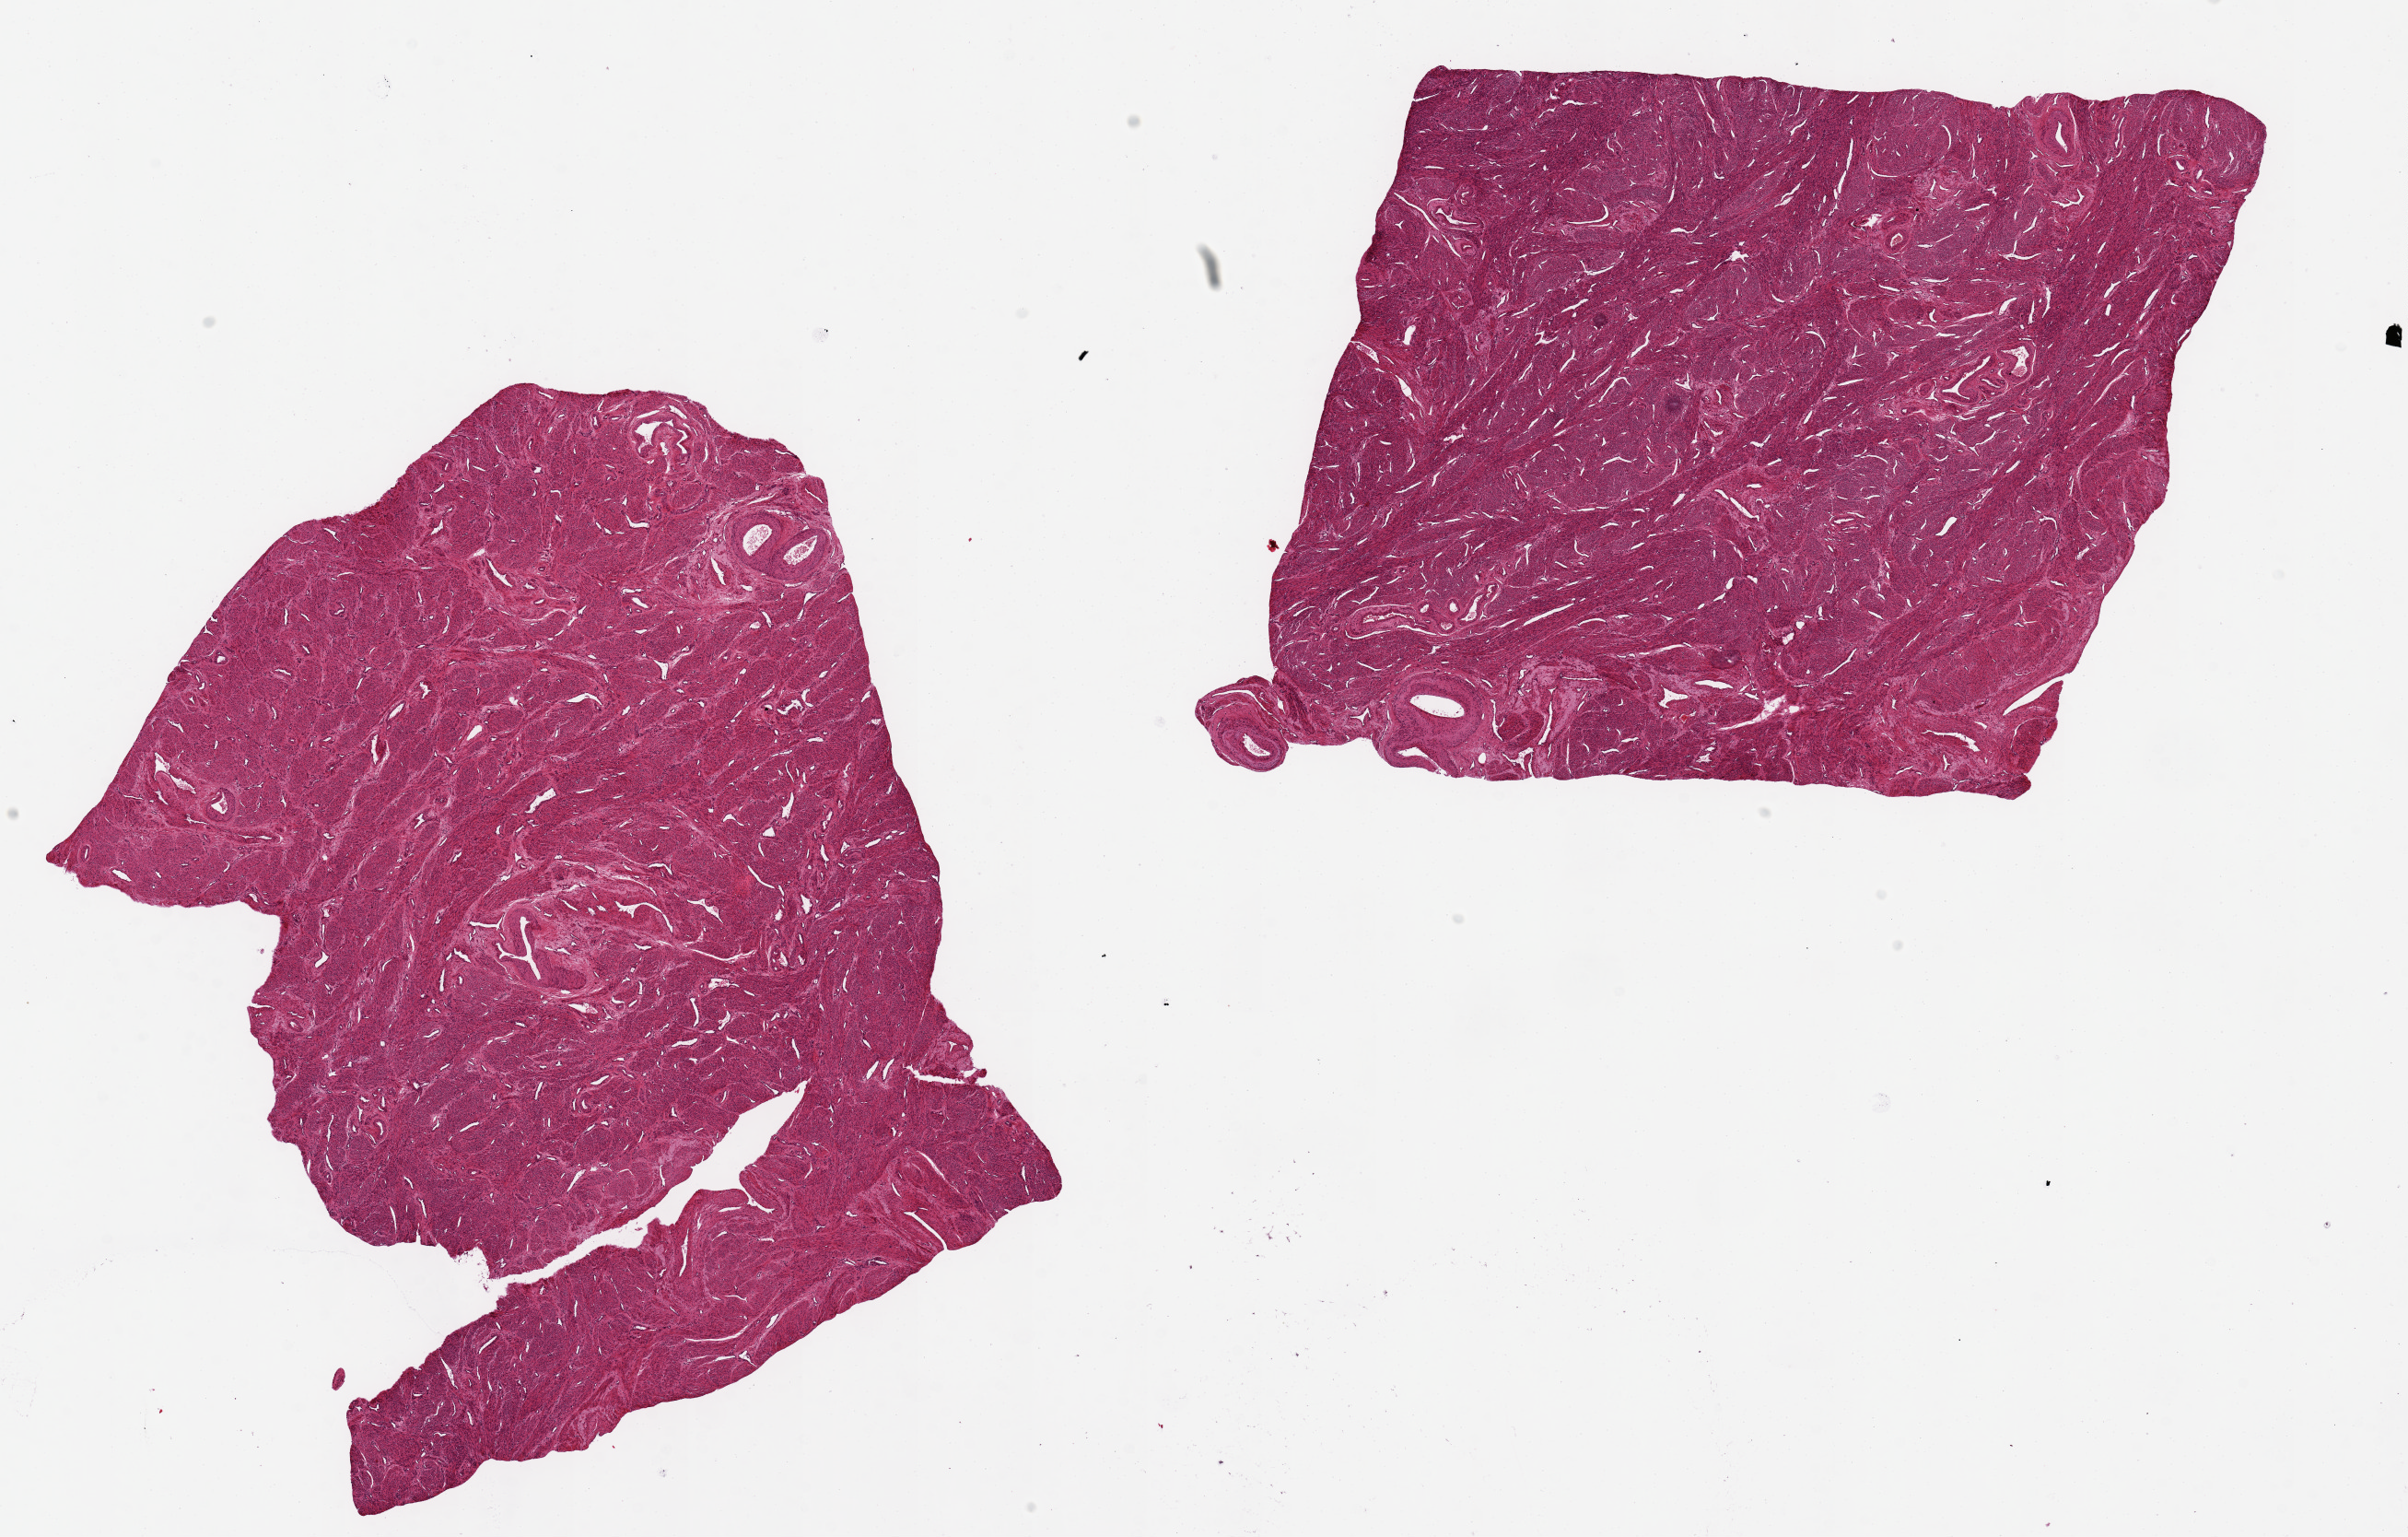
Haematoxylin and eosin whole-slide image — whole scanned area (about 20.7 x 13.2 mm, slide scanned at 20x) shown as a low-resolution overview, PAXgene-fixed paraffin-embedded (PFPE) section, target tissue: uterus, donor tissue sample. Donor sex: female.
Review note (as recorded): 2 pieces ~7x7mm. All myometrium; no endometrial elements noted.